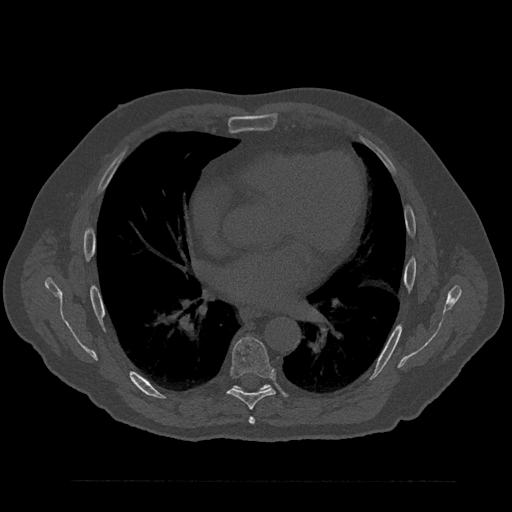
CT including the spine, one axial slice. Slice 498 of 797 in the series (ordered by position). 120 kVp. Bone window (W 1800 / L 400 HU). 0.5 mm slice thickness. 512 × 512 image matrix, field of view 430 × 430 mm. Male patient, age 61 years. Case-level facts recorded for this patient, not image findings: primary cancer: prostate.
Annotated regions visible in this slice (semi-automatic segmentation, software-assisted and operator-edited):
- T6 vertebra: box from (x=249, y=417) to (x=255, y=424) px
- T7 vertebra: (x=228, y=337)–(x=275, y=410)
- T8 vertebra: (x=233, y=384)–(x=270, y=391)